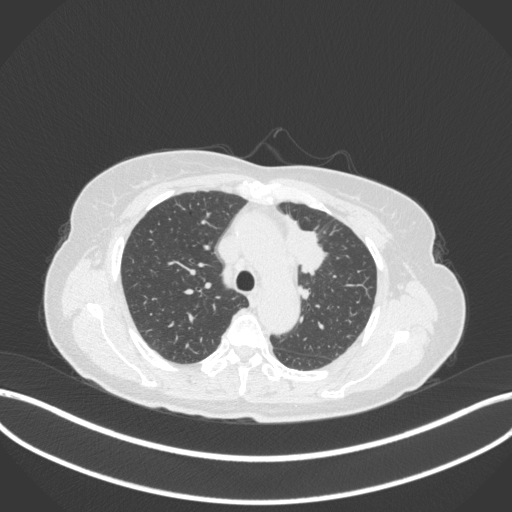
Chest CT, one axial slice. 120 kVp. Lung window (W 1500 / L -600 HU). 512 × 512 image matrix. Female patient, age 65 years. Case-level facts recorded for this patient, not image findings: clinical TNM (as recorded): T2a N0 M0; histopathological grade: G2-3.
Outlined on this slice (bounding box drawn by a radiologist):
- lung tumour (recorded histology: adenocarcinoma): bounding box [x1, y1, x2, y2] px = [282, 214, 330, 278]